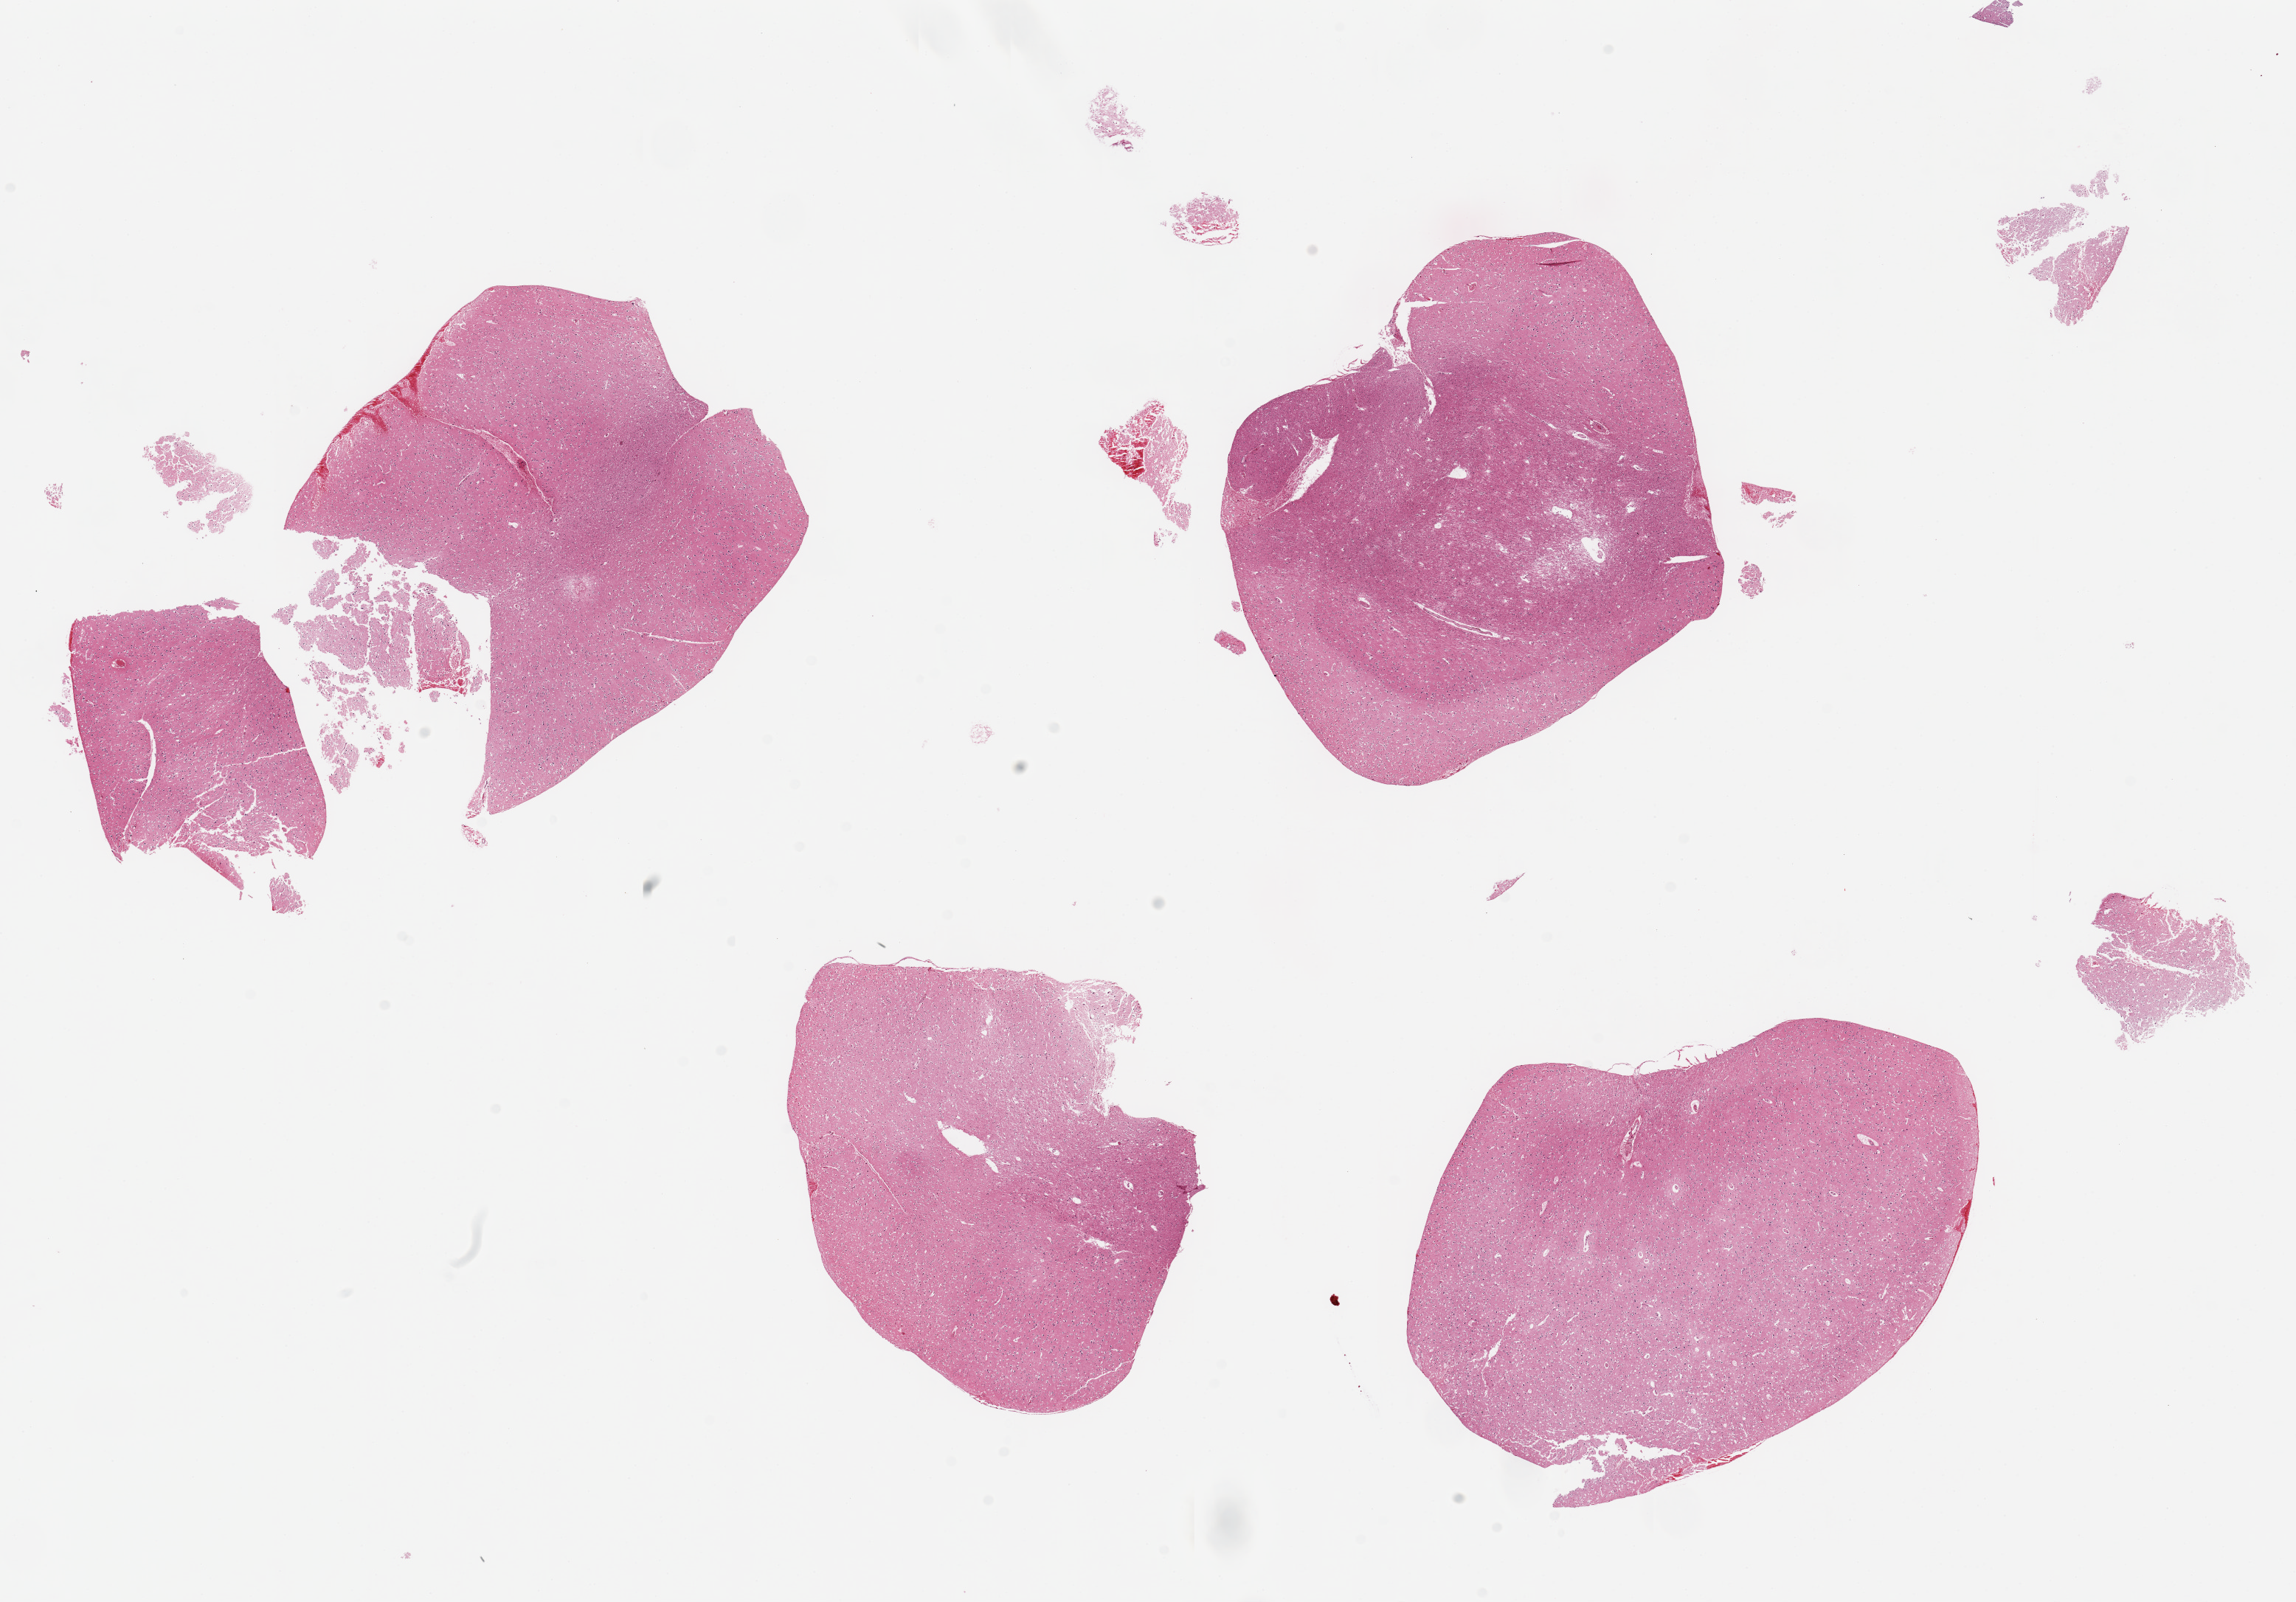
Hematoxylin and eosin (H&E) whole-slide image, shown as a low-resolution overview of the whole scanned area (about 24.6 x 17.2 mm); PAXgene-fixed, paraffin-embedded tissue; sampled site (target tissue): cerebral cortex; tissue donor sample. Donor sex: male.
• reviewer comment on this tissue sample: 4 pieces, up to 8x5.5mm